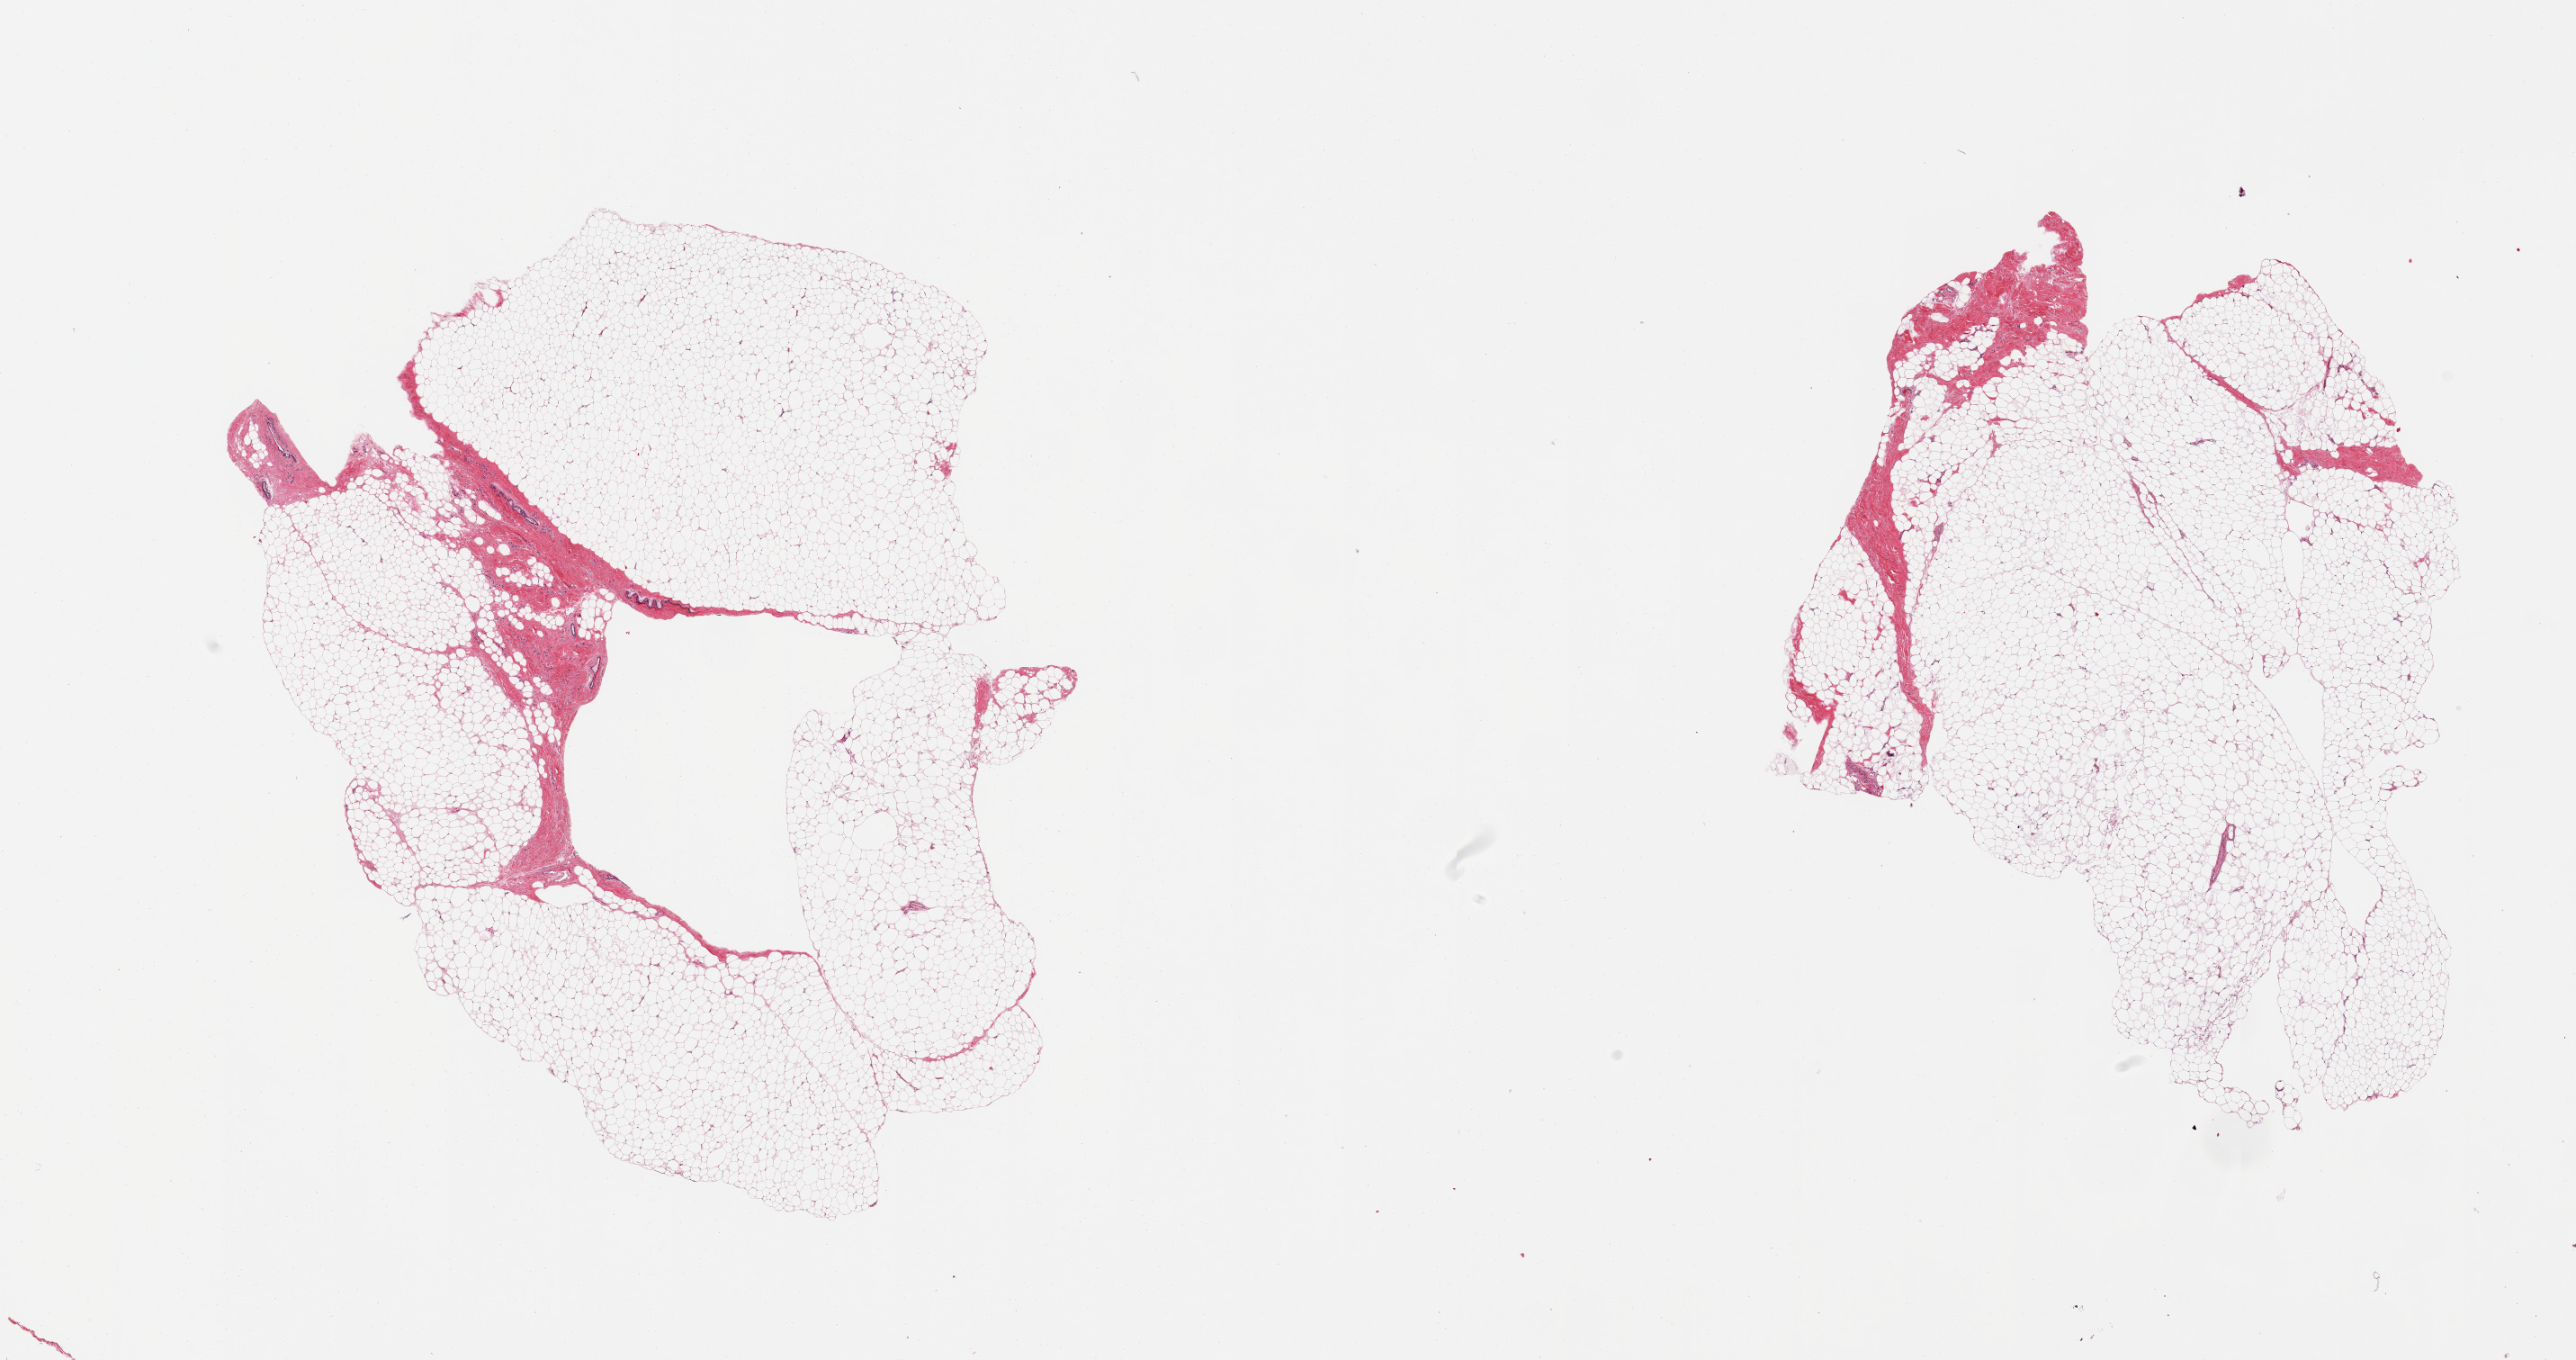
Whole-slide image, H&E stain, brightfield, low-resolution overview of the scanned area, about 22.6 x 11.9 mm (slide scanned at 20x). PAXgene-fixed paraffin-embedded (PFPE) section. Section of breast (target tissue). Donor tissue sample. Donor sex: male.
* pathologist's review note for this sample: 2 pieces, mainly fibroadipose elements; trace ducts